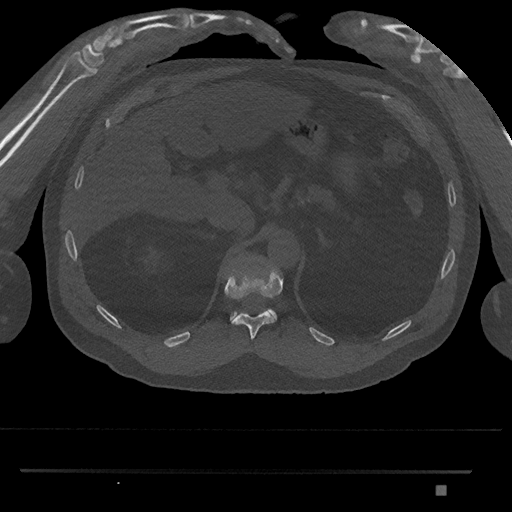
CT including the spine, one axial slice. Position 932 of 1134 along the scan axis. Bone window (W 1800 / L 400 HU). 0.5 mm slice thickness. 512 × 512 image matrix, field of view 429 × 429 mm. Male patient, age 65 years. From the clinical record (not read from this slice): primary cancer: prostate.
Annotated regions visible in this slice (semi-automatically segmented with operator editing):
- T11 vertebra: bounding box (x1, y1, x2, y2) in pixels: (224, 270, 283, 340)
- T12 vertebra: (230, 309, 277, 321)